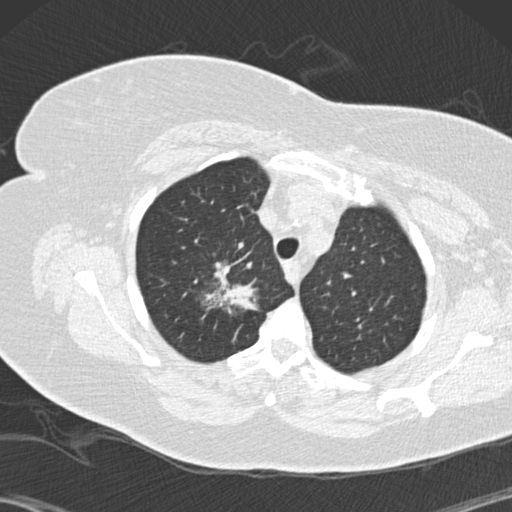
Low-dose screening chest CT, one axial slice. Position 117 of 146 along the scan axis. 120 kVp. Lung window (W 1500 / L -600 HU). 2 mm slice thickness. 512 × 512 image matrix, field of view 350 × 350 mm.
Outlined on this slice (outlined manually by an expert reader):
- lesion 1 (tumor, upper lobe of right lung): bounding box [x1, y1, x2, y2] px = [205, 267, 256, 312]